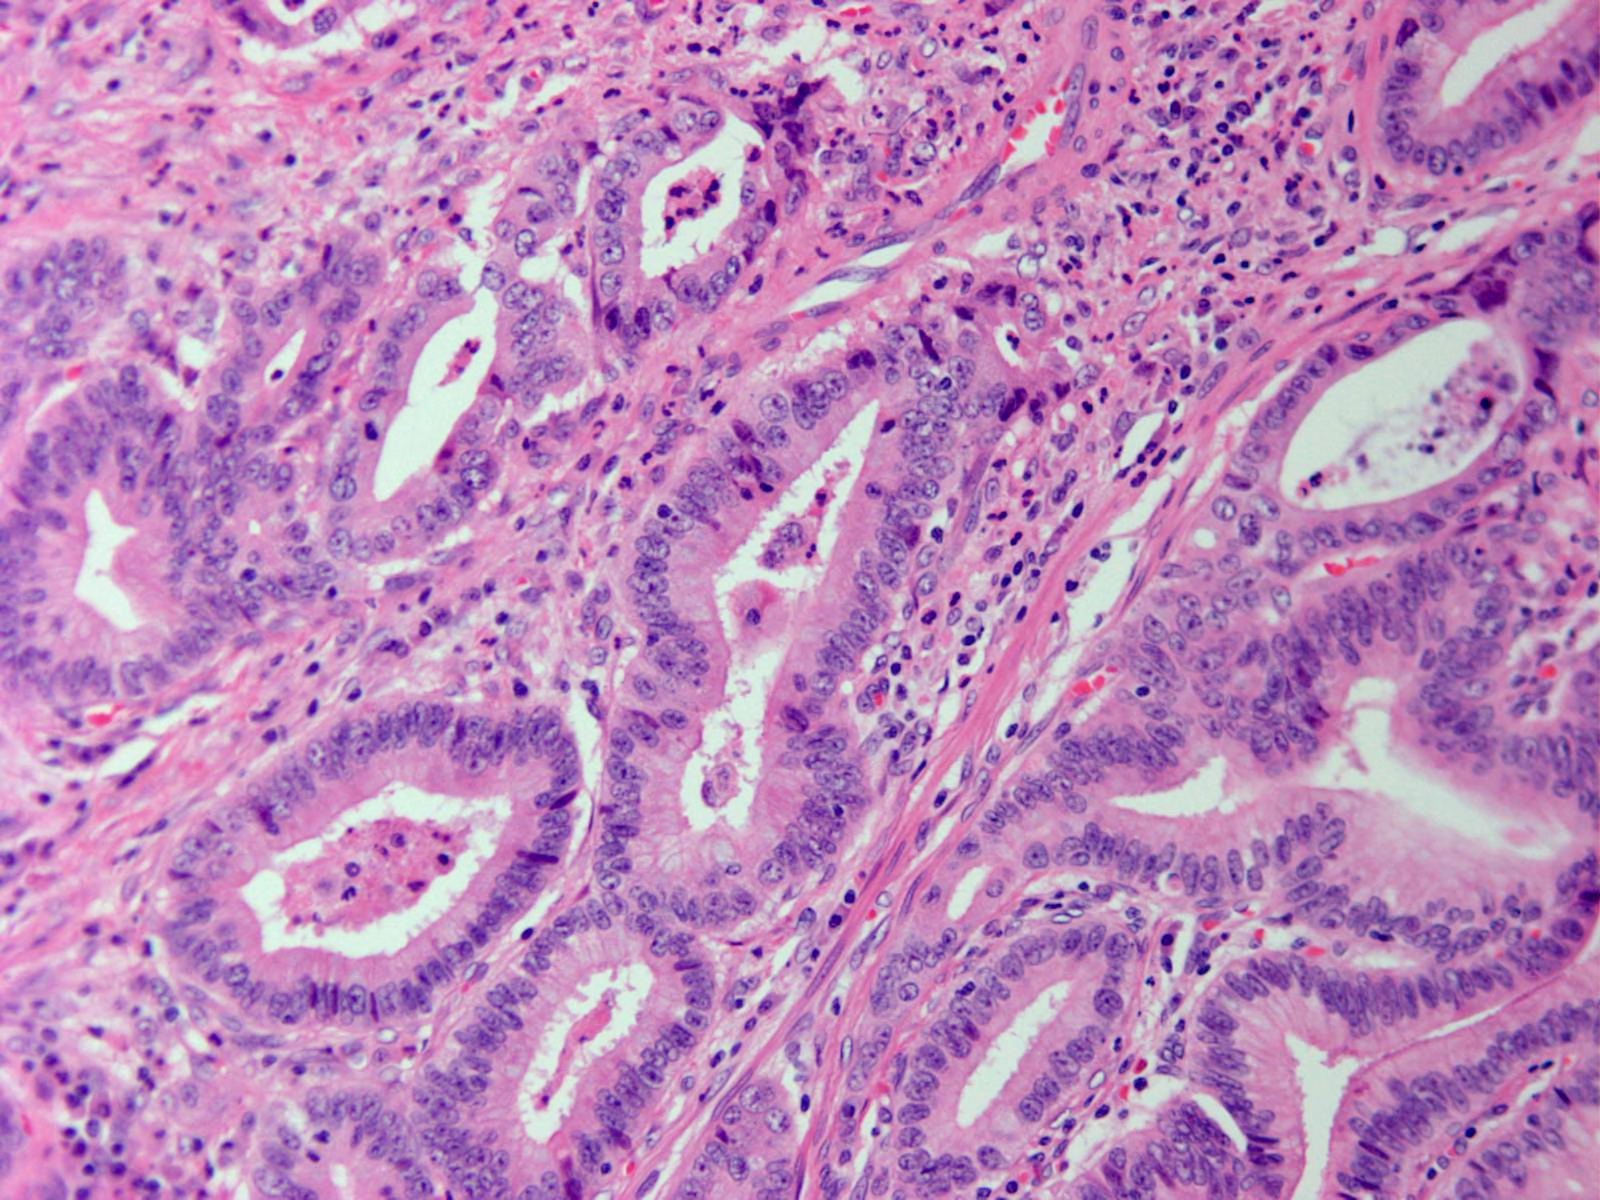
Single-field H&E photomicrograph, covering about 0.8 x 0.6 mm; FFPE section; sample: primary tumour, stomach. Male, age 51 years at initial diagnosis. Histologic grade: G2 (moderately differentiated).
AJCC pathologic stage: IB (6th edition). TNM: T2a N0 M0. Histologic diagnosis: Adenocarcinoma, NOS (body of stomach). Lymph nodes positive (case pathology): 0 of 6 examined.